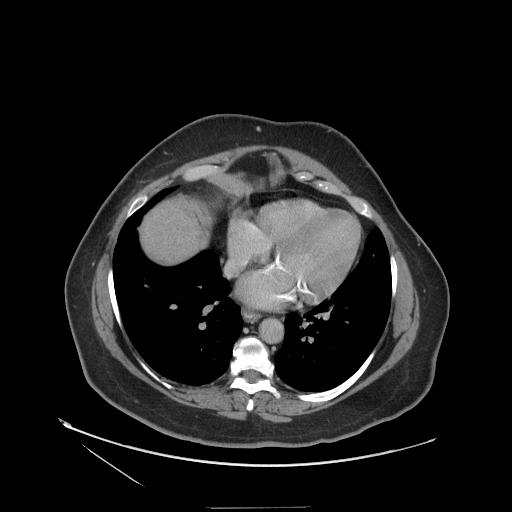
Contrast-enhanced abdominal CT (liver protocol), one axial slice; reconstruction kernel STANDARD; 140 kVp; soft-tissue window (W 400 / L 40 HU); 2.5 mm slice thickness; 512 × 512 image matrix, field of view 480 × 480 mm. From the clinical record (not read from this slice): diagnosis: hepatocellular carcinoma (patient treated with transarterial chemoembolisation; whether this scan precedes or follows treatment is not stated here); TNM stage (as recorded): Stage-II; Child-Pugh class: A; tumour differentiation: well differentiated.
Structures marked on this image (semi-automatic segmentation, software-assisted and operator-edited):
- liver parenchyma outside the tumour (the mass and vessels are separate outlines, so this box may not span the whole liver): bounding box <140,198,208,263> (left, top, right, bottom; pixels)